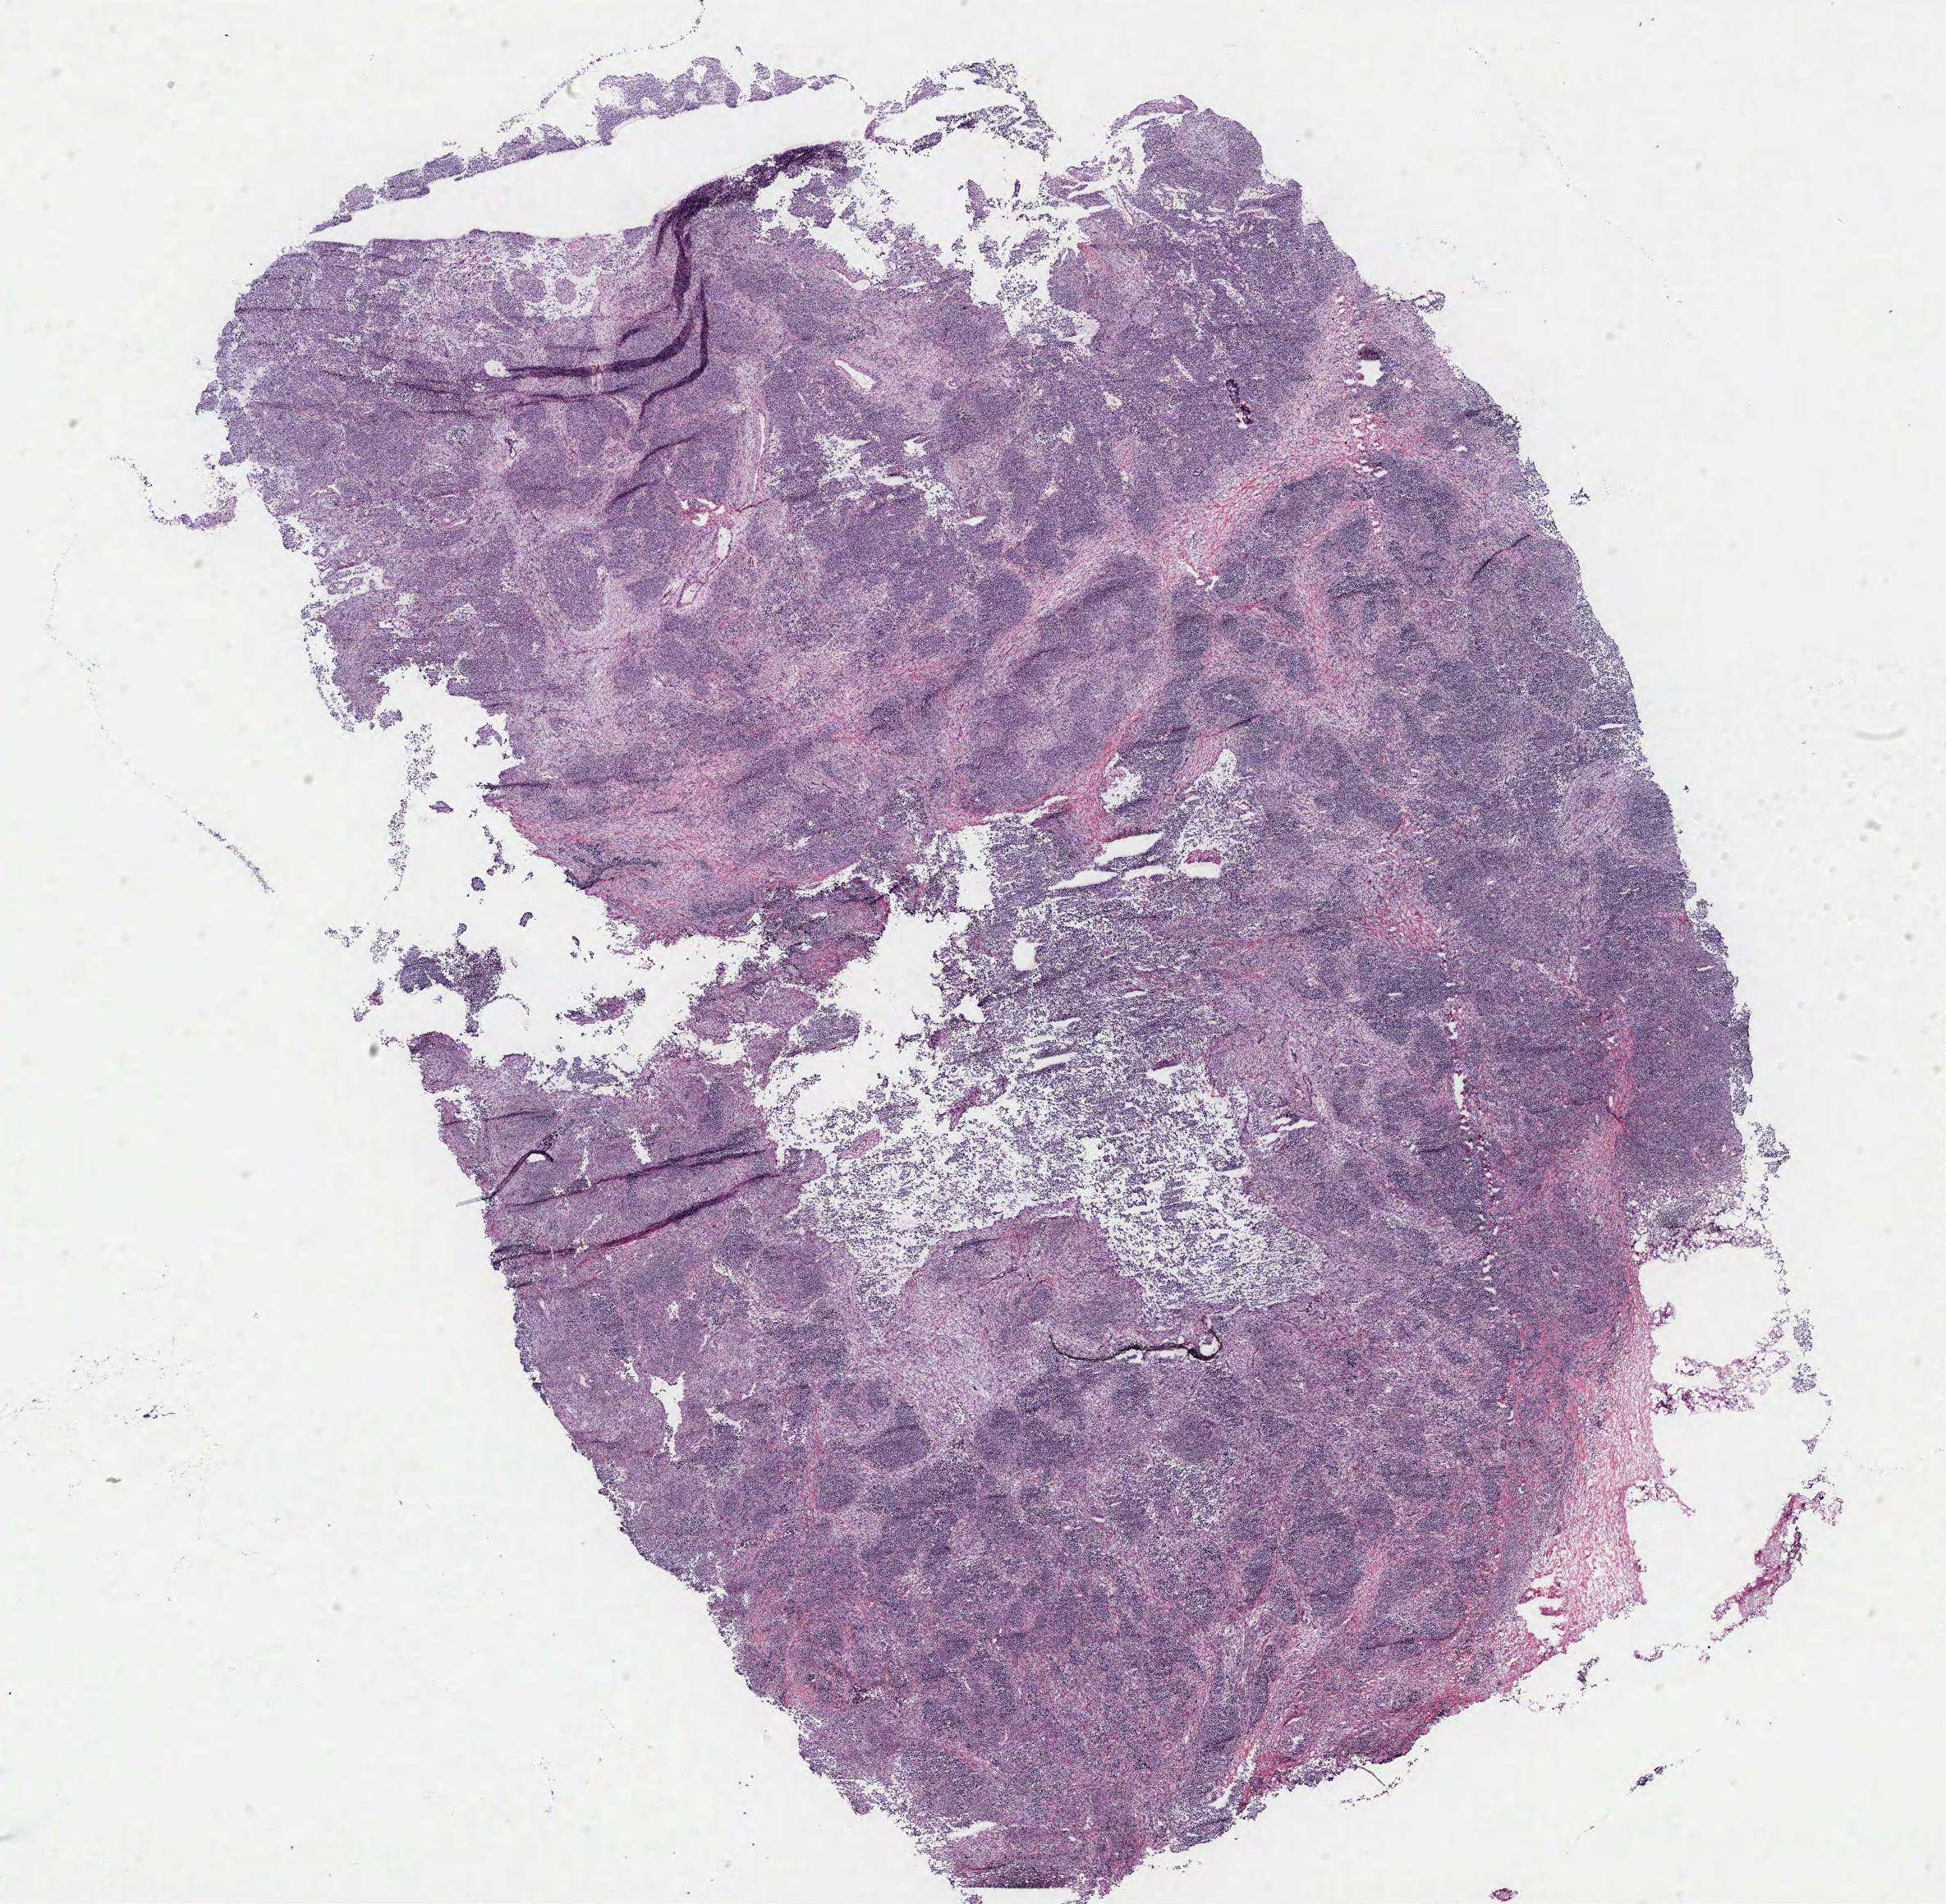
Digitized Hematoxylin and eosin (H&E) stained tissue section (whole slide), a low-resolution overview of the entire scanned area, about 19.0 x 18.6 mm (slide scanned at 40x). Breast, tissue type not recorded. Female, 80 y/o.
Patient diagnosis: Infiltrating duct carcinoma, NOS.